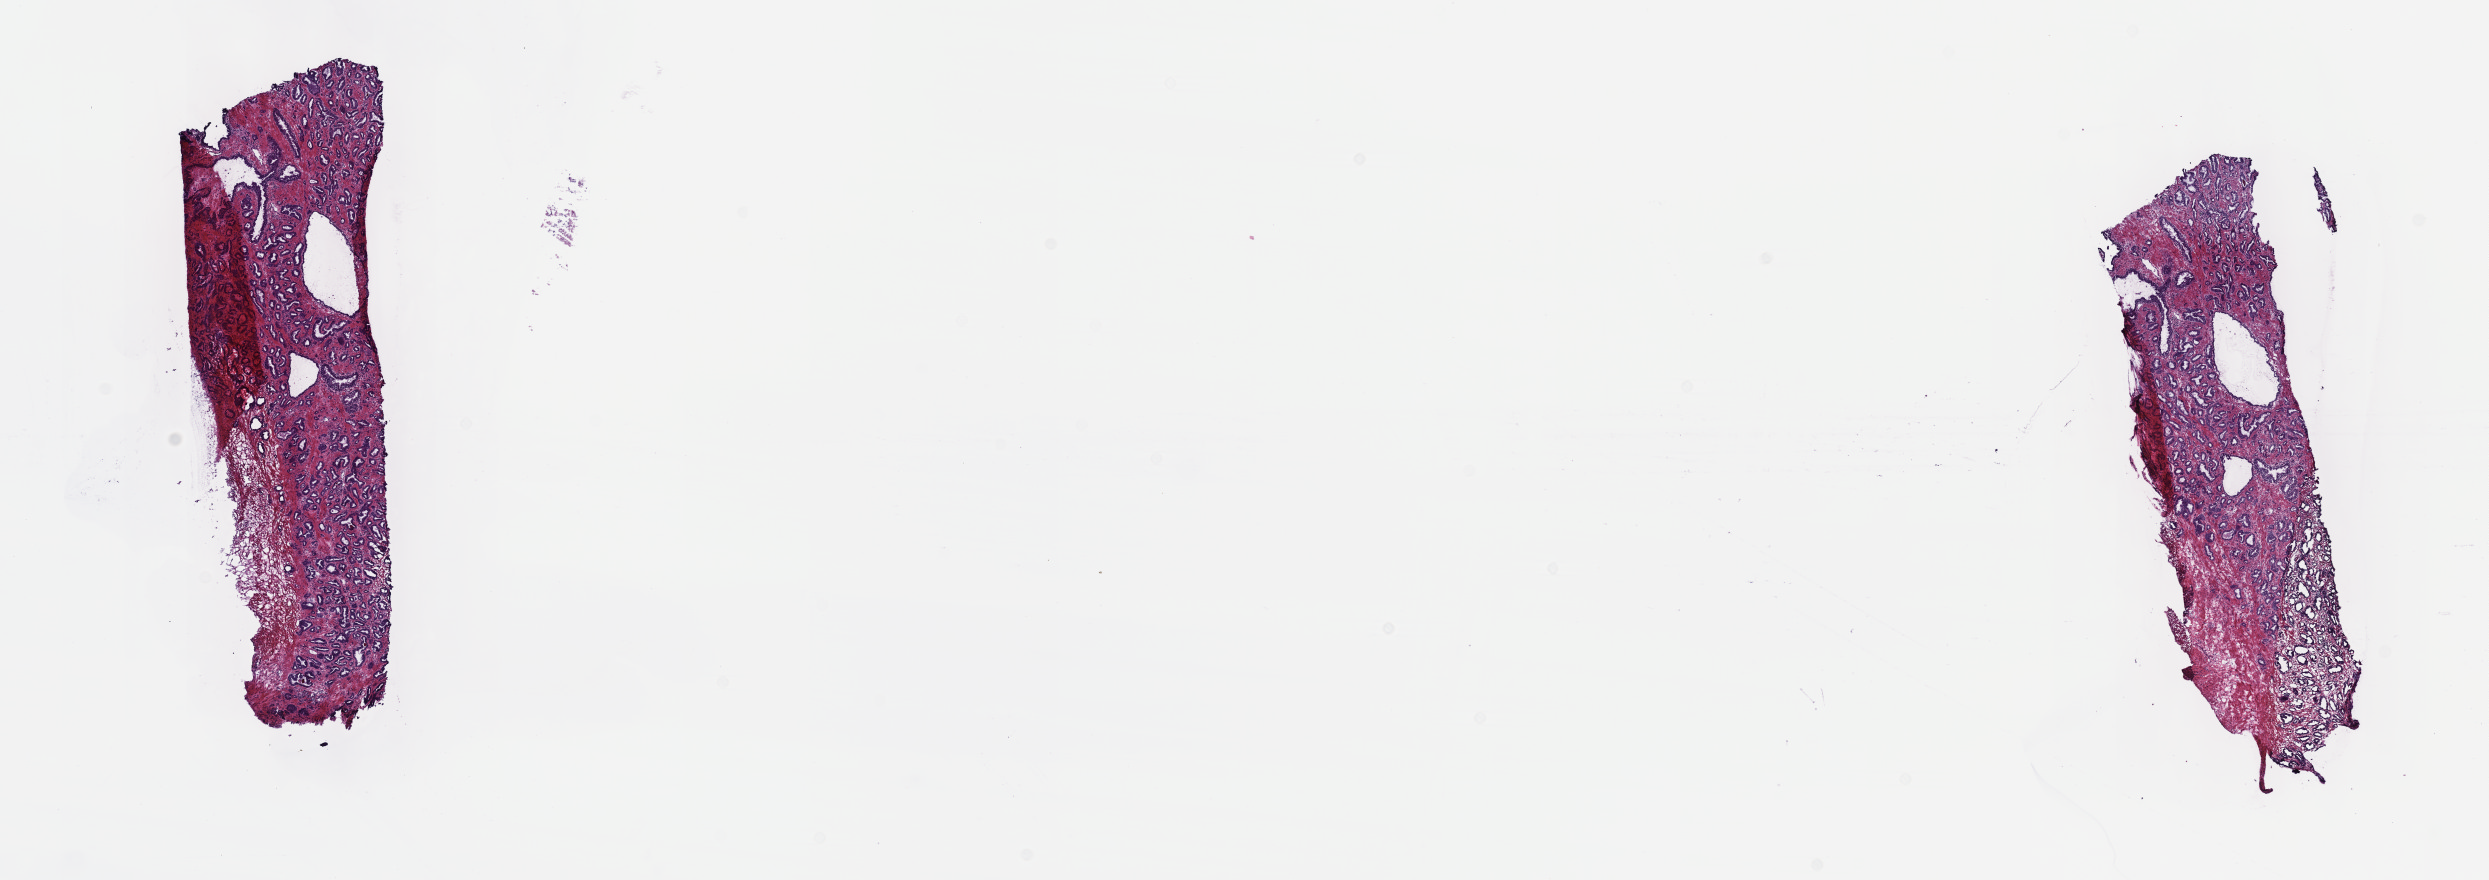
Digitized H&E-stained tissue section (whole slide), a low-resolution overview of the entire scanned area, about 20.1 x 7.1 mm. Frozen section from the top of the tissue portion. Primary tumour sample from the prostate. Male patient; age at initial diagnosis 47 years. Gleason score: 6 (3+3). Slide review estimates, as recorded: tumour cells 75%, tumour nuclei 75%, normal cells 5%, stromal cells 20%, necrosis 0%. Inflammatory infiltration, as recorded: lymphocyte infiltration 3%, monocyte infiltration 1%, neutrophil infiltration 1%.
Pathologic diagnosis: Adenocarcinoma, NOS (prostate gland).